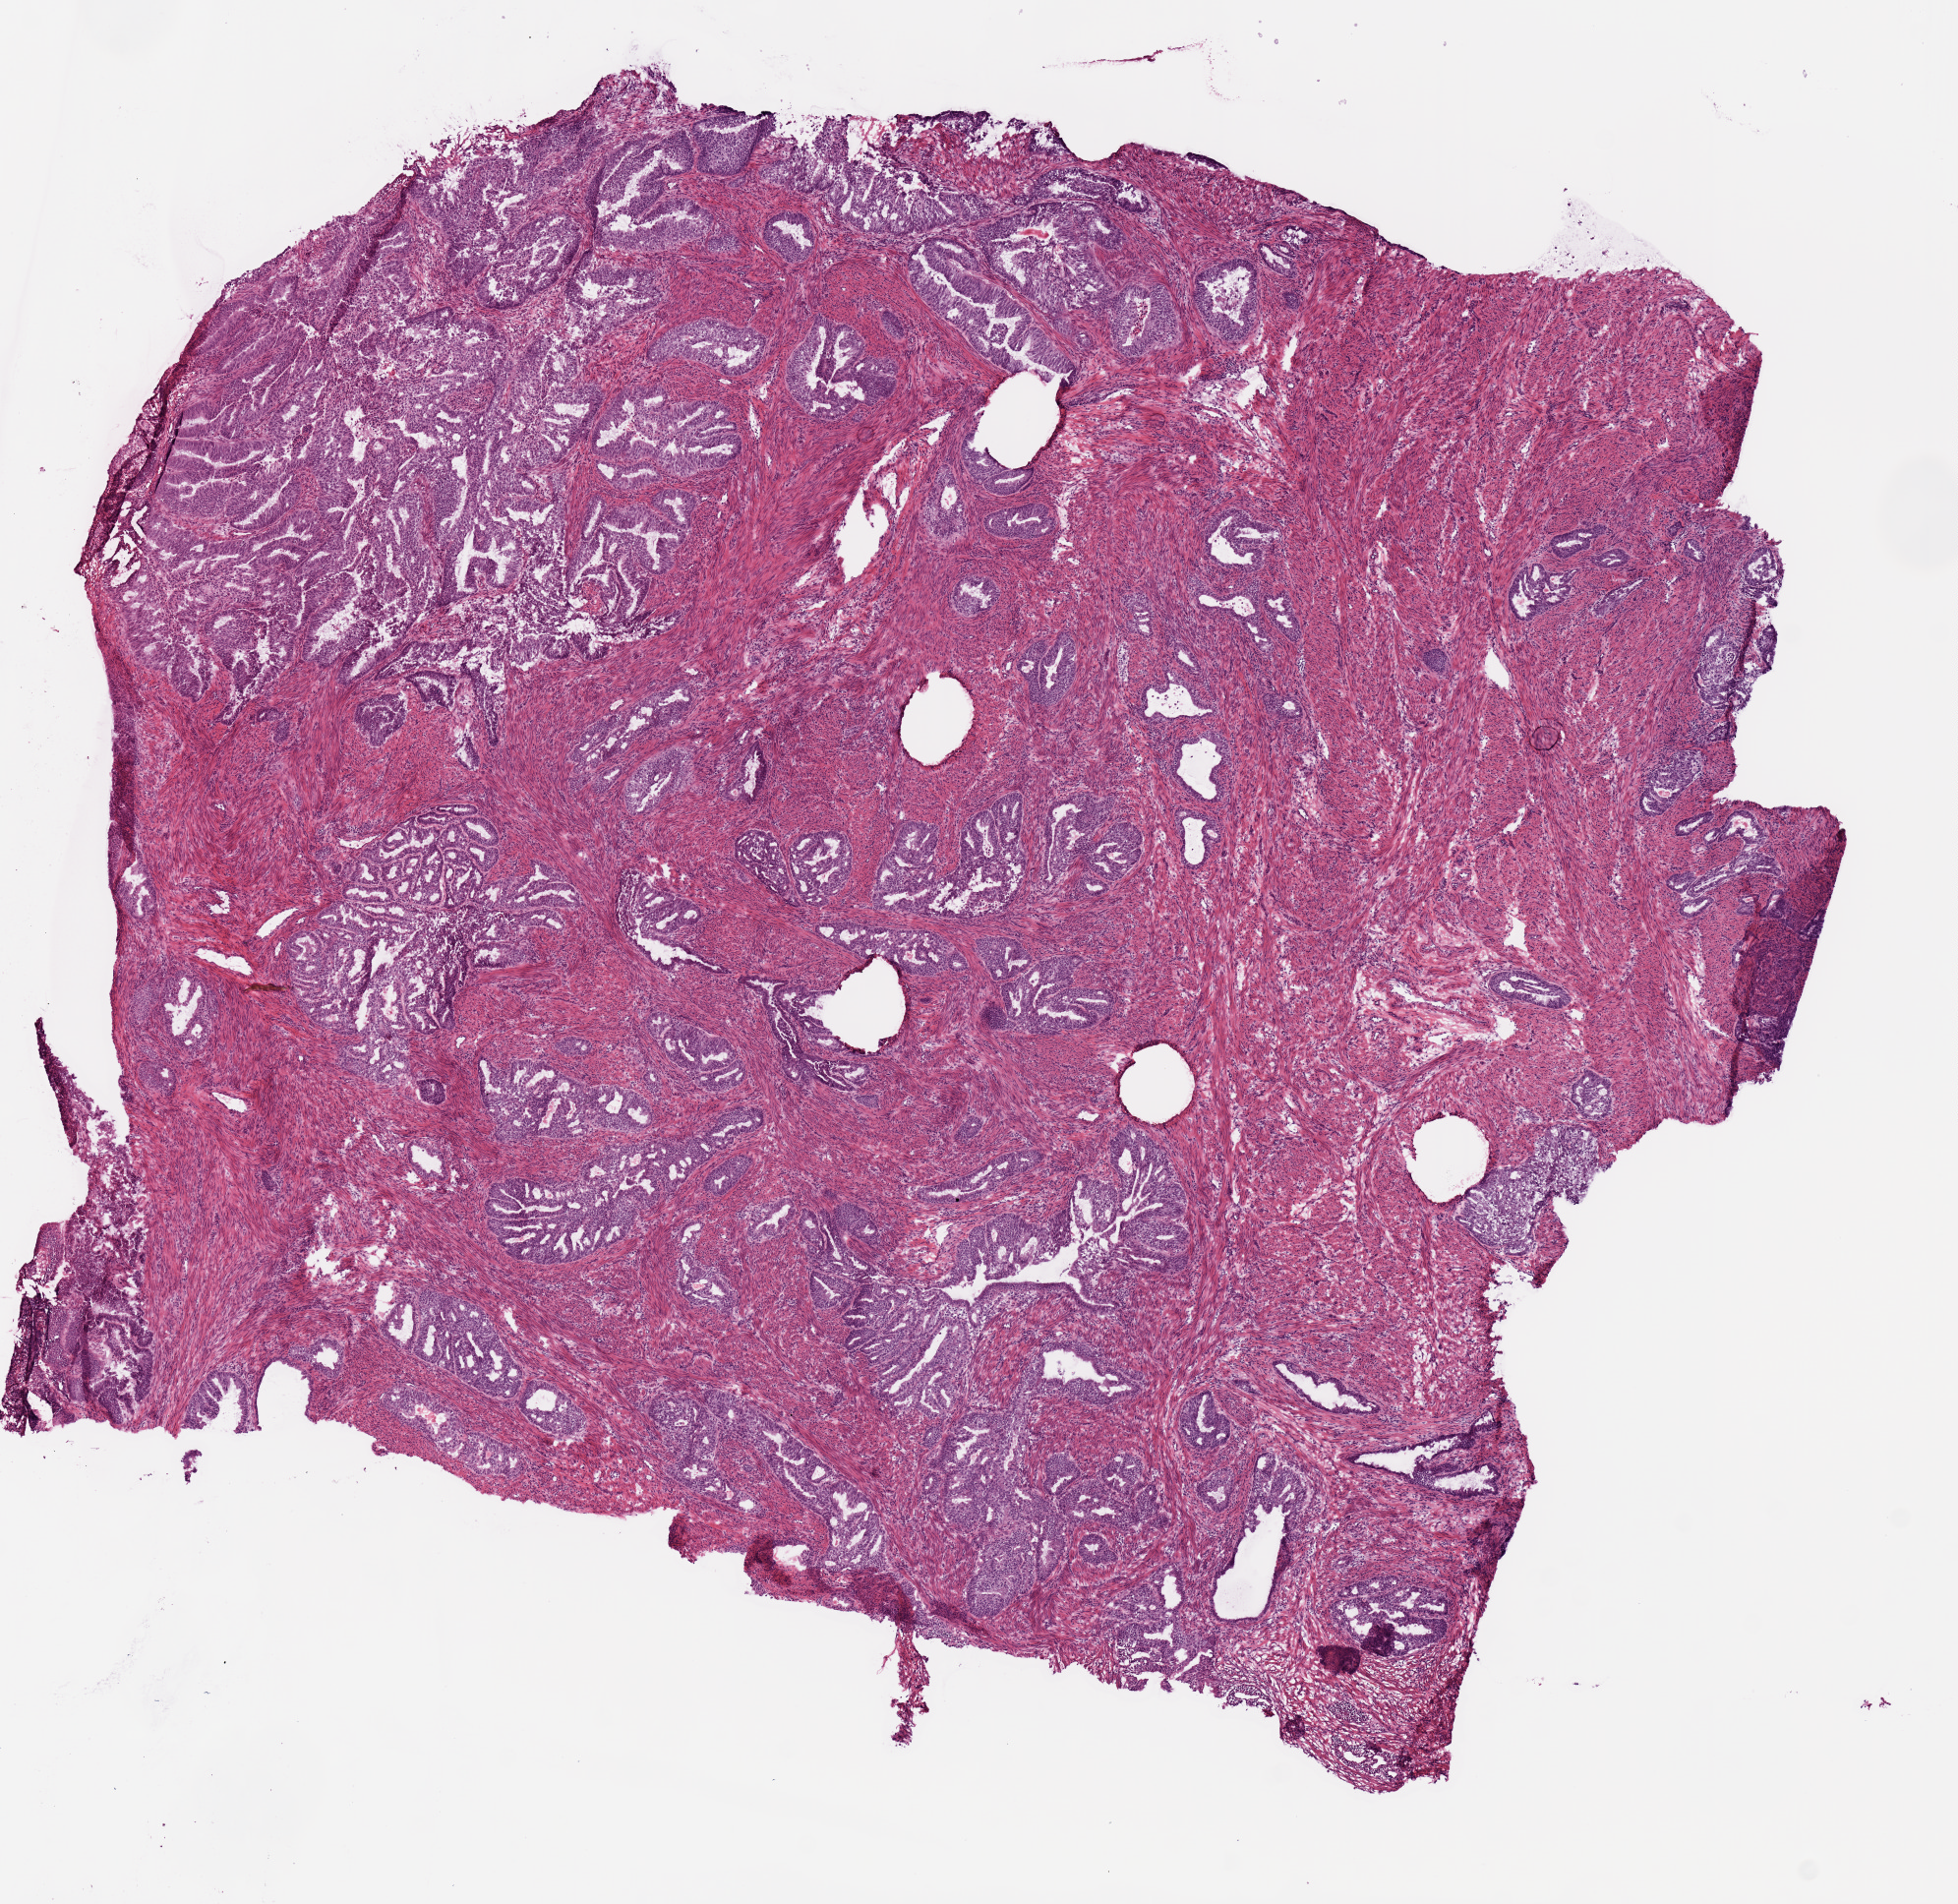
Digitized H&E-stained tissue section (whole slide), low-resolution overview of the scanned area, about 7.9 x 7.7 mm (slide scanned at 20x), frozen section from the top of the tissue portion, sample: primary tumour, uterus. Female, age 60 years at initial diagnosis. Histologic grade: G3 (poorly differentiated). Composition of this section per pathologist review: tumour cells 75%, tumour nuclei 75%, normal cells 0%, stromal cells 15%, necrosis 10%. Infiltration values recorded for this section: lymphocyte infiltration 0%, monocyte infiltration 0%, neutrophil infiltration 0%.
Diagnosis: Endometrioid adenocarcinoma, NOS. FIGO stage: II.